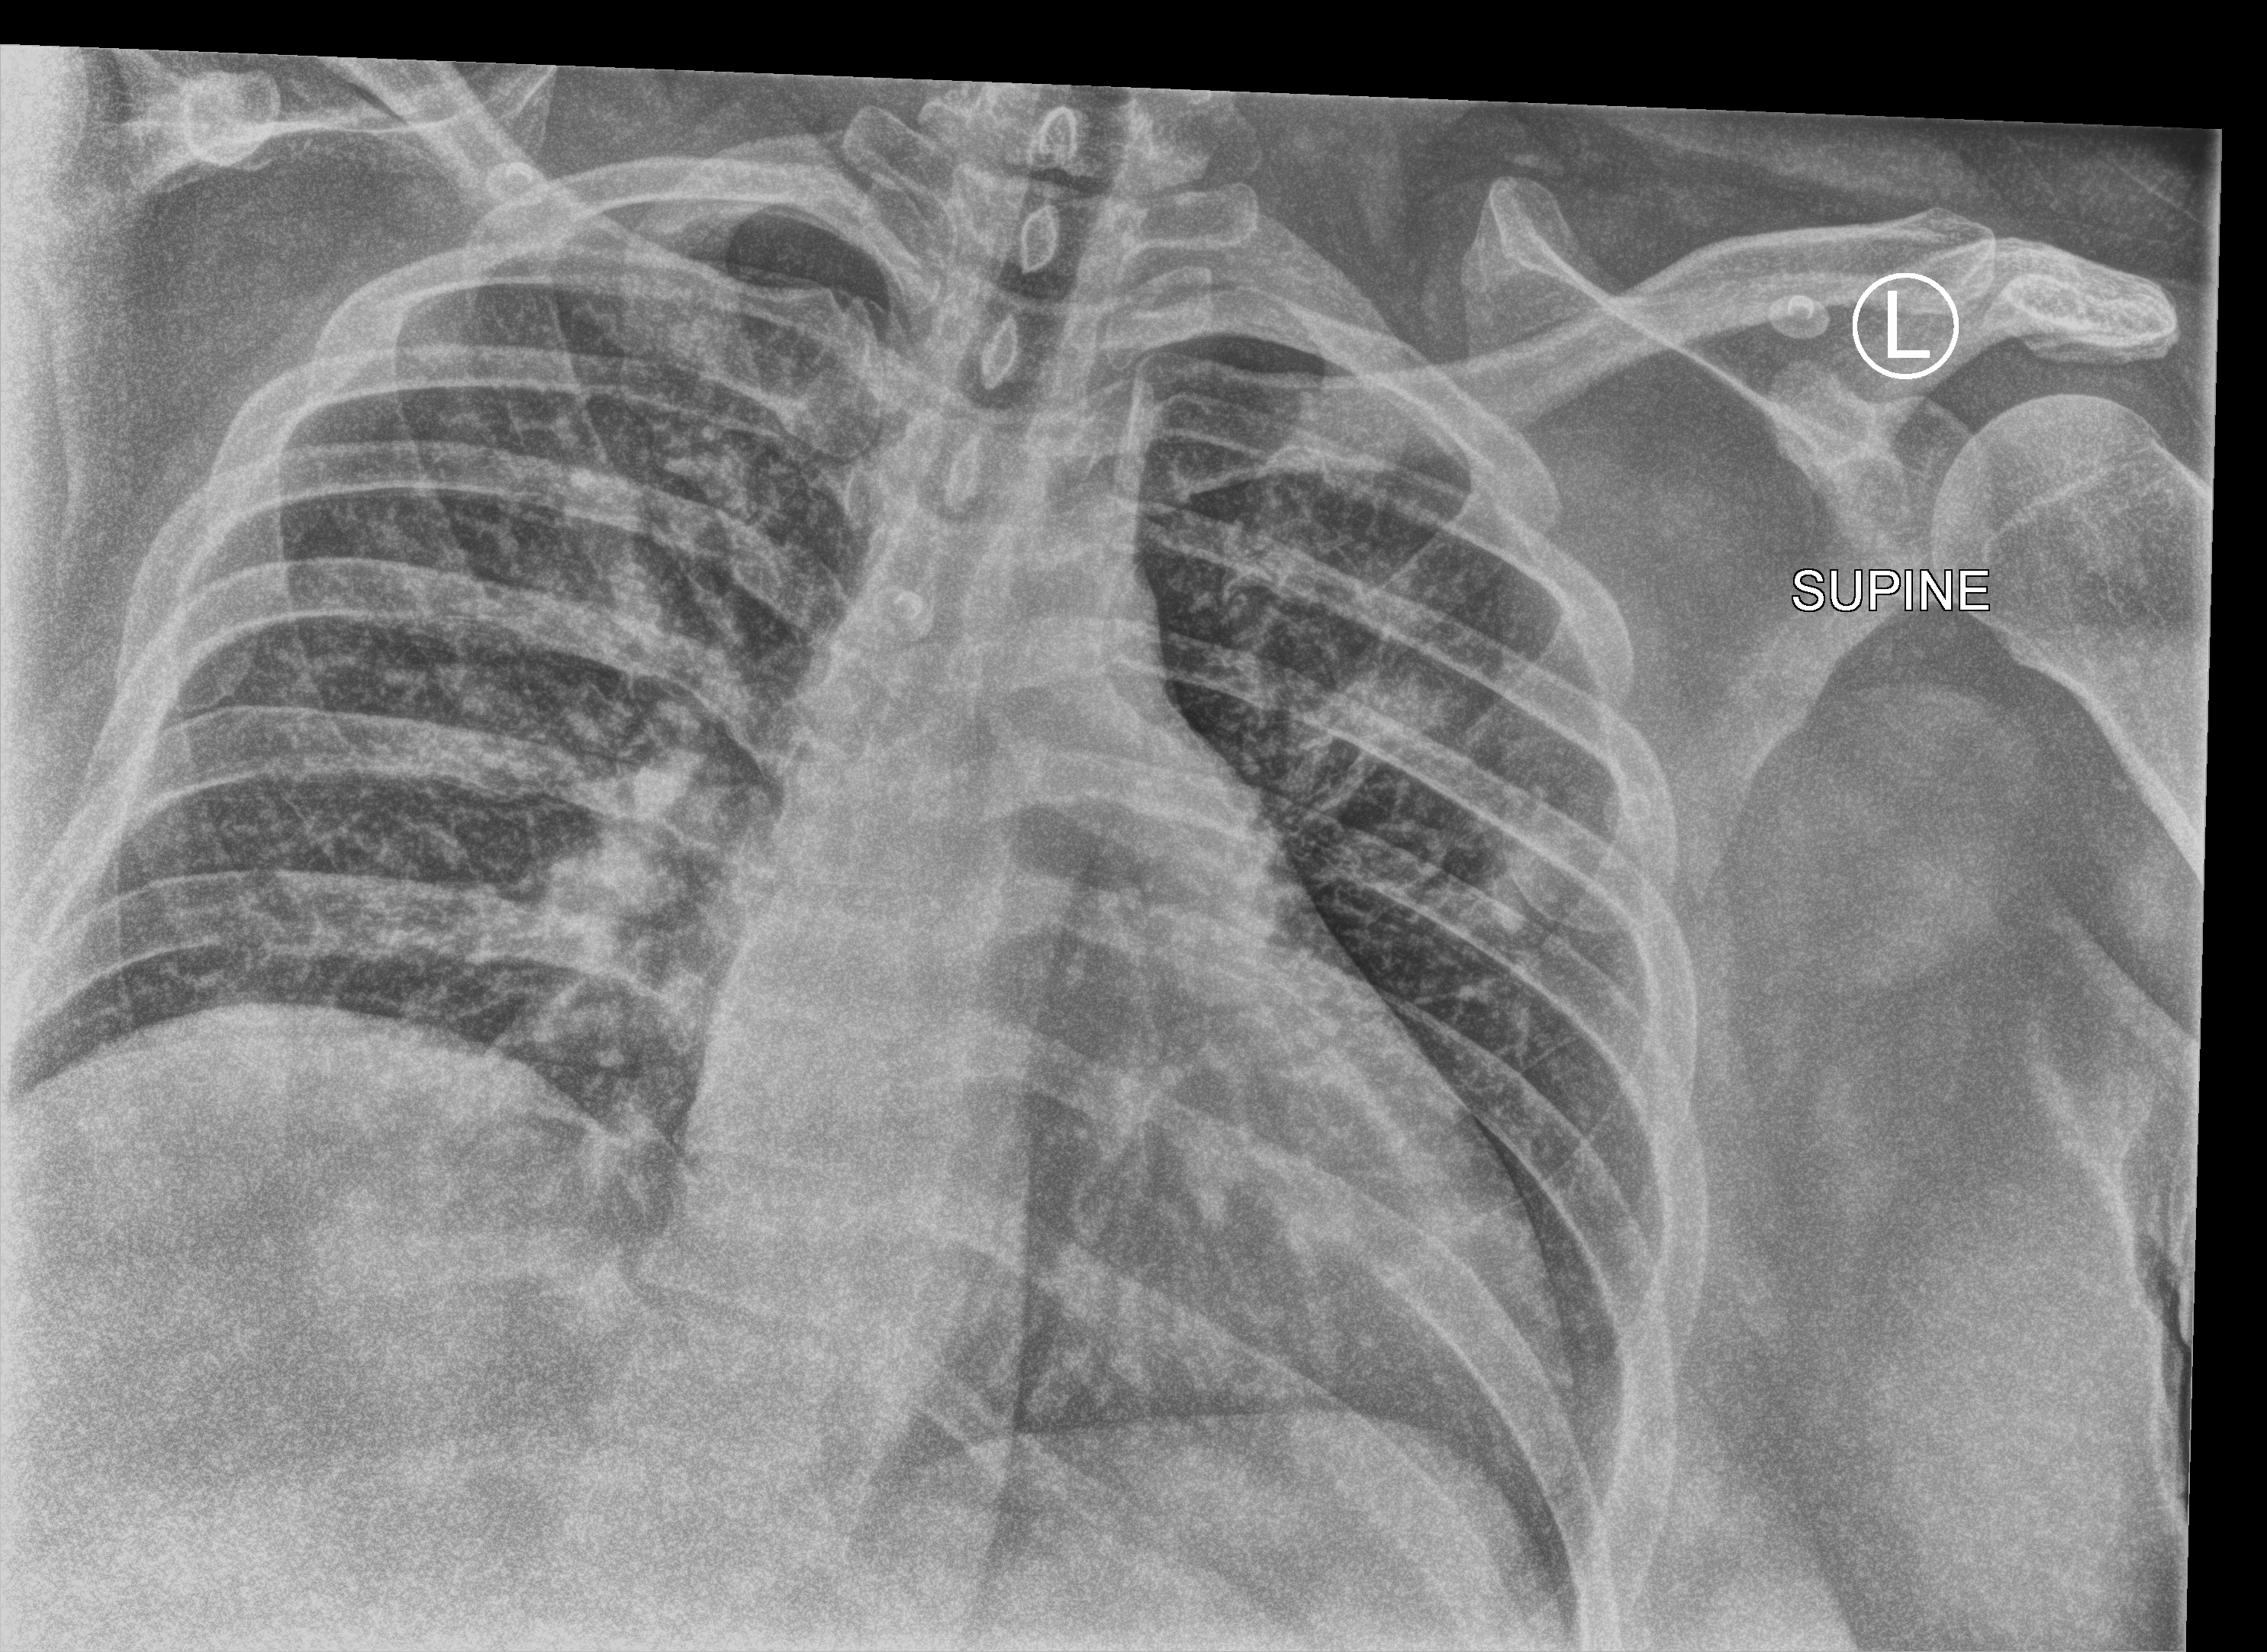
Bedside chest radiograph (computed radiography); anteroposterior (AP) projection. Patient hospitalised with COVID-19; female, aged 18–59 years.
From the hospital-stay record, not from the radiograph (when in the stay this image was taken is not recorded): hypertension (admission record): yes; smoking status (admission record): never; admitted to intensive care during this hospital stay: no.